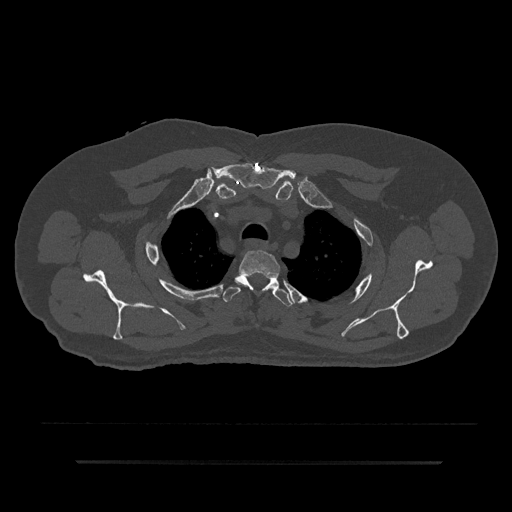
CT including the spine, one axial slice; slice 677 of 797 in the series (ordered by position); reconstruction kernel Br40s/3; 120 kVp; bone window (W 1800 / L 400 HU); 0.5 mm slice thickness; 512 × 512 image matrix, field of view 464 × 464 mm. Male patient, age 59 years. From the clinical record (not read from this slice): primary cancer: bile ducts.
Outlined on this slice (semi-automatic segmentation, software-assisted and operator-edited):
- T2 vertebra: box from (x=237, y=250) to (x=280, y=293) px
- T3 vertebra: (x=223, y=274)–(x=294, y=307)